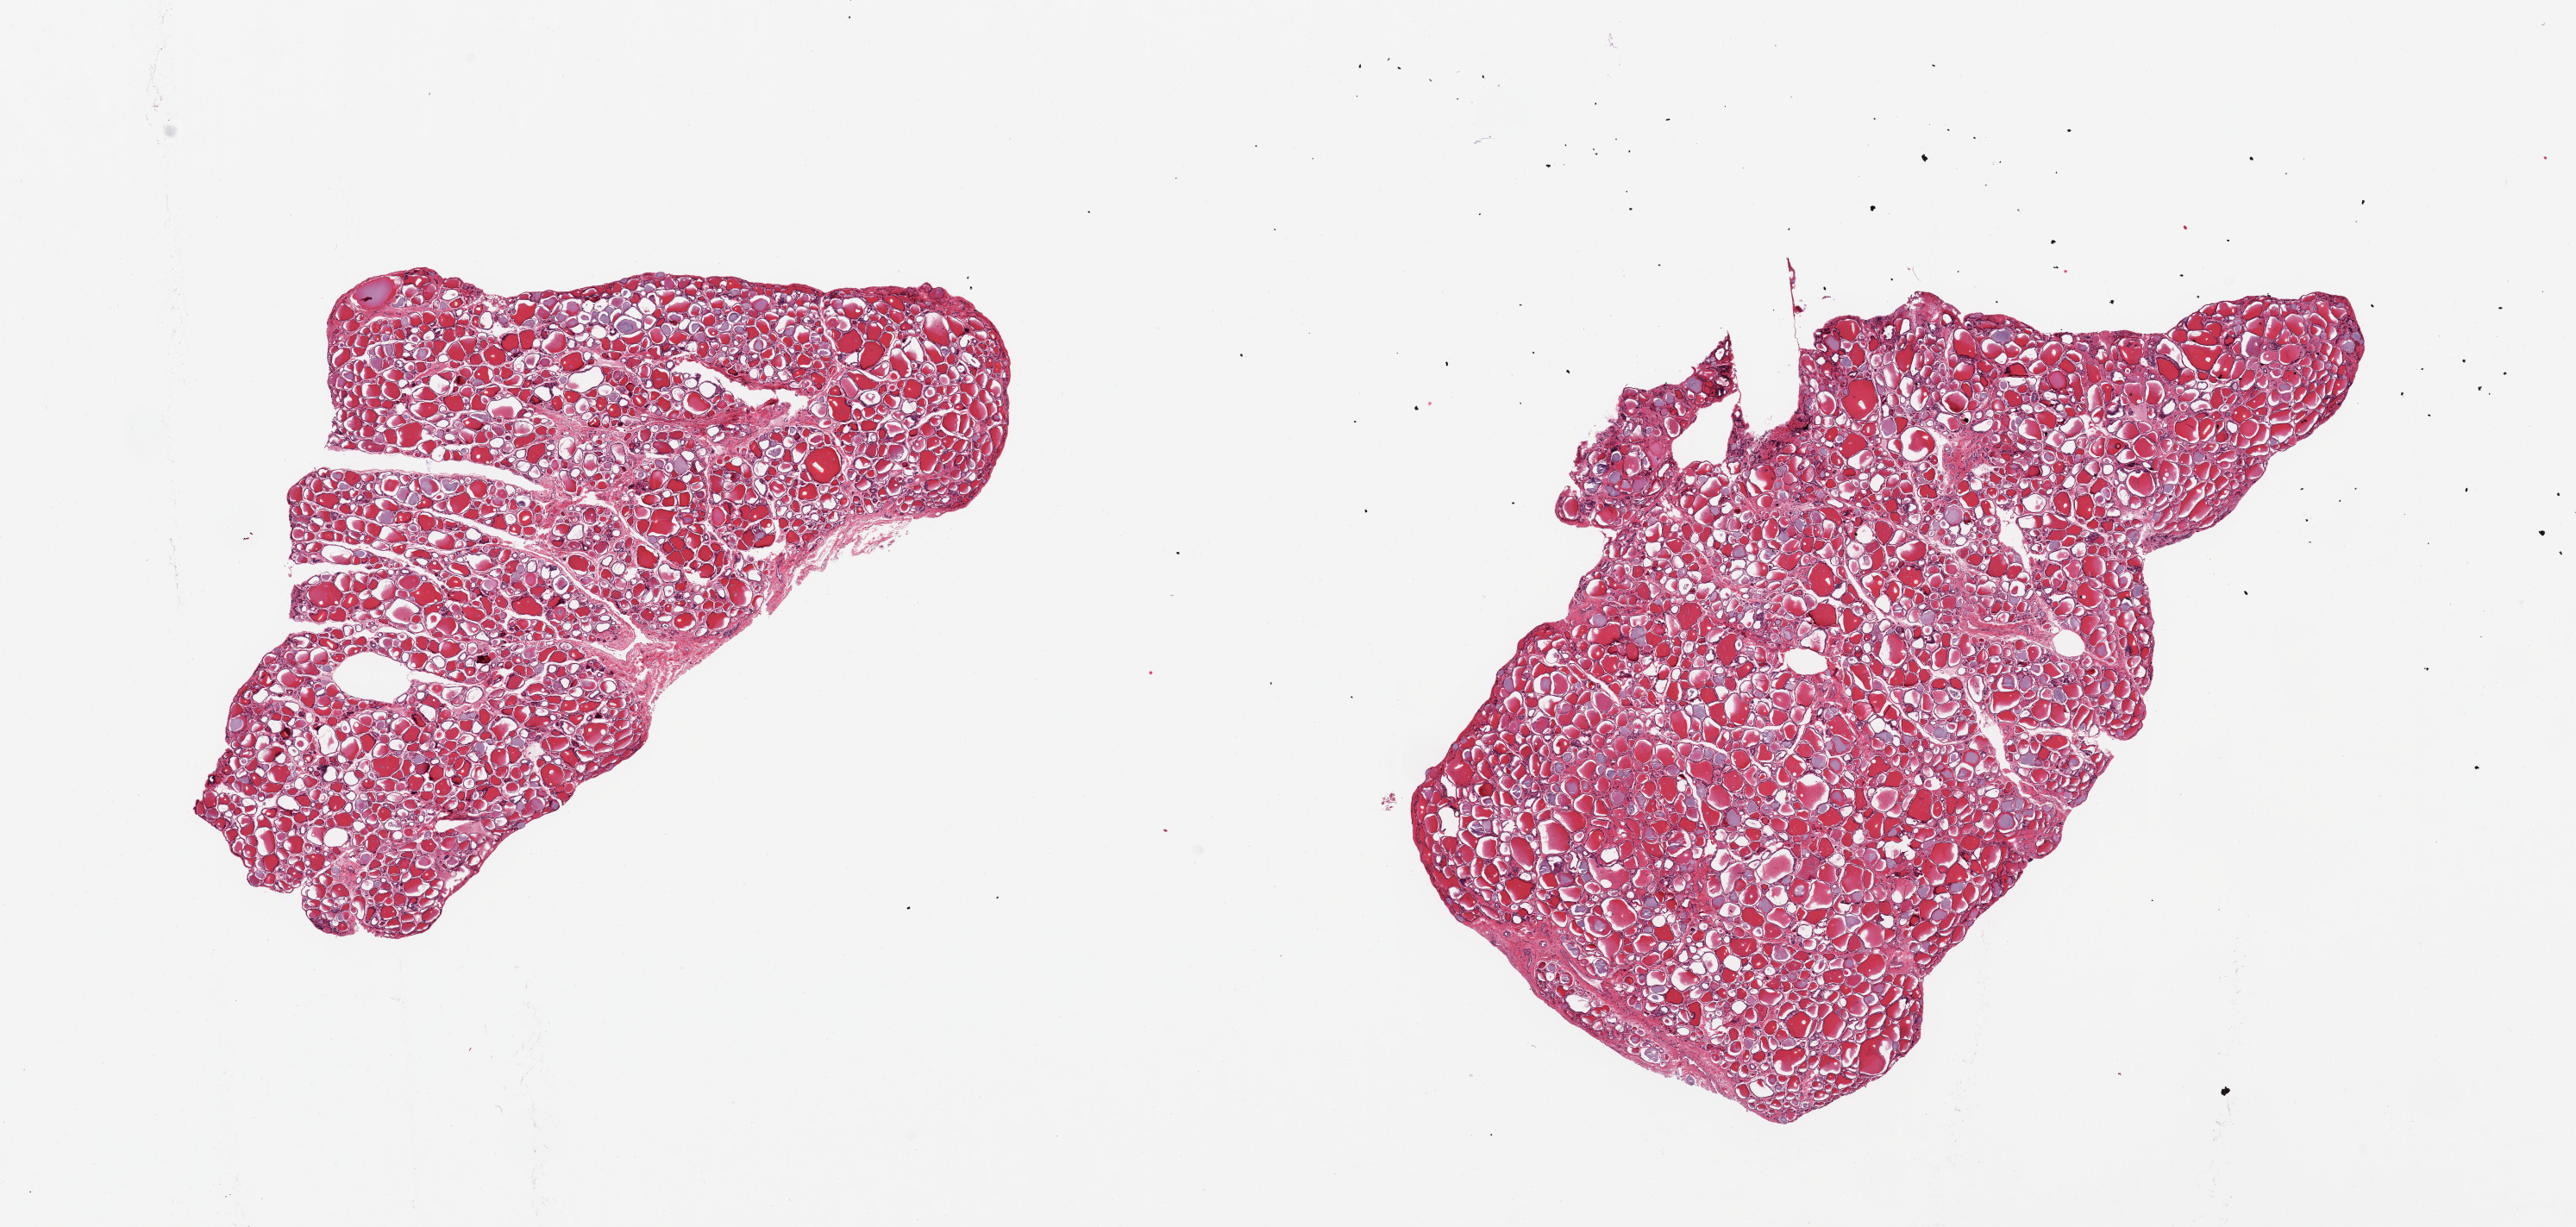
Digitized H&E-stained section — low-resolution overview of the scanned area, about 23.6 x 11.3 mm (acquisition: 20x scan); PAXgene-fixed, paraffin-embedded tissue; target tissue: thyroid; donor tissue sample. Donor sex: male.
* pathologist's review note for this sample: 2 pieces; no lesions; well dissected